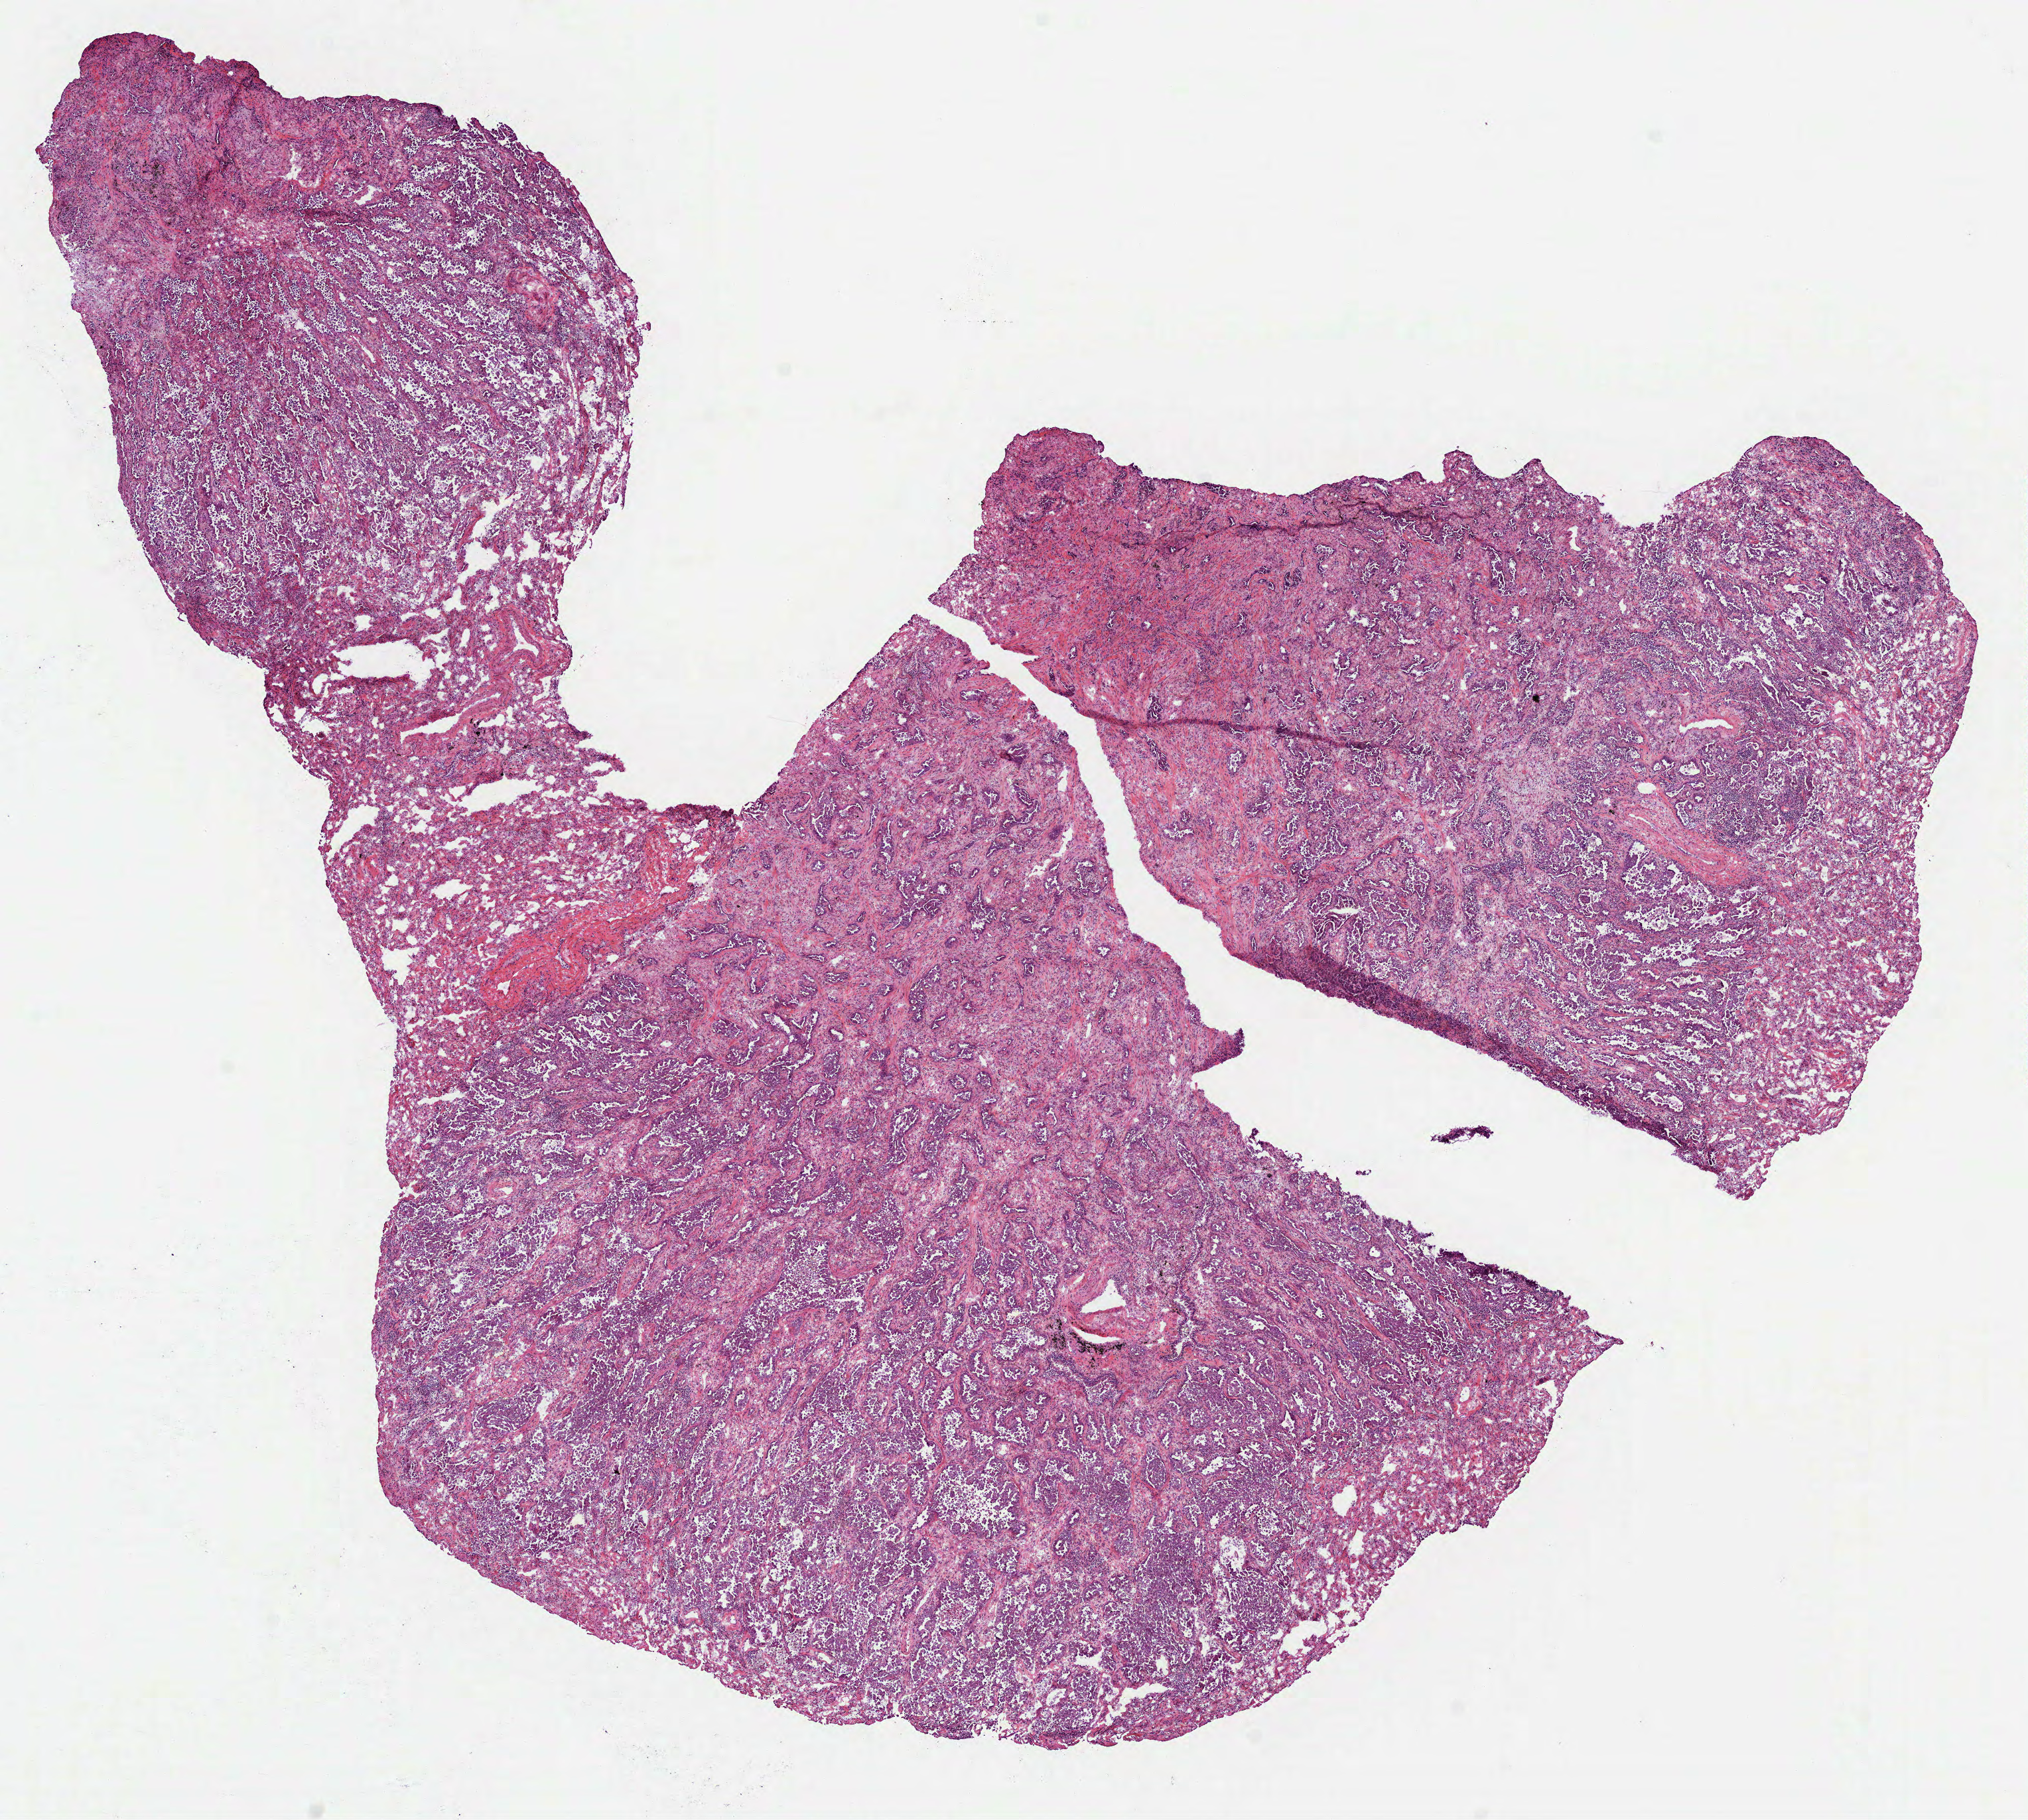
Digitized Hematoxylin and eosin (H&E) stained tissue section (whole slide) — a low-resolution overview of the entire scanned area, about 12.3 x 11.1 mm (acquisition: 40x scan), frozen section, sample: primary tumour, lung. Female patient; age at initial diagnosis 74 years. Pathologist review of this section (percent, as recorded): tumour cells 70%, tumour nuclei 60%, normal cells 10%, stromal cells 20%, necrosis 0%.
* AJCC pathologic stage: IIIA (7th edition)
* histologic diagnosis: Bronchiolo-alveolar carcinoma, non-mucinous (lower lobe, lung)